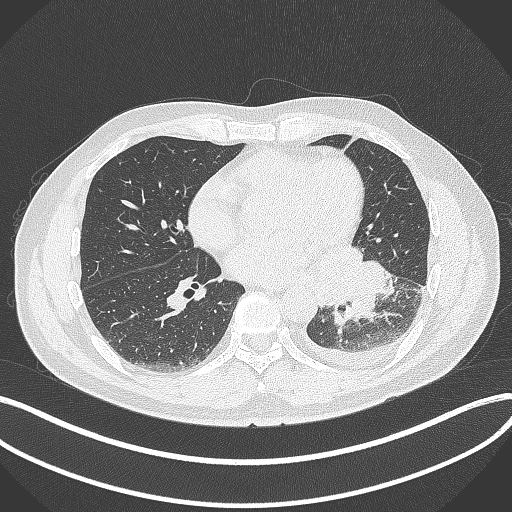
Chest CT, one axial slice; slice 154 of 342 in the series (ordered by position); reconstruction kernel B70f; 120 kVp; lung window (W 1500 / L -600 HU); 1 mm slice thickness; 512 × 512 image matrix. Male patient, age 58 years. From the clinical record (not read from this slice): clinical TNM (as recorded): T3 N1 M1b.
Outlined on this slice (rectangle marked by the reading radiologist):
- lung tumour (recorded histology: small cell carcinoma): bounding box (x1, y1, x2, y2) in pixels: (319, 243, 392, 329)